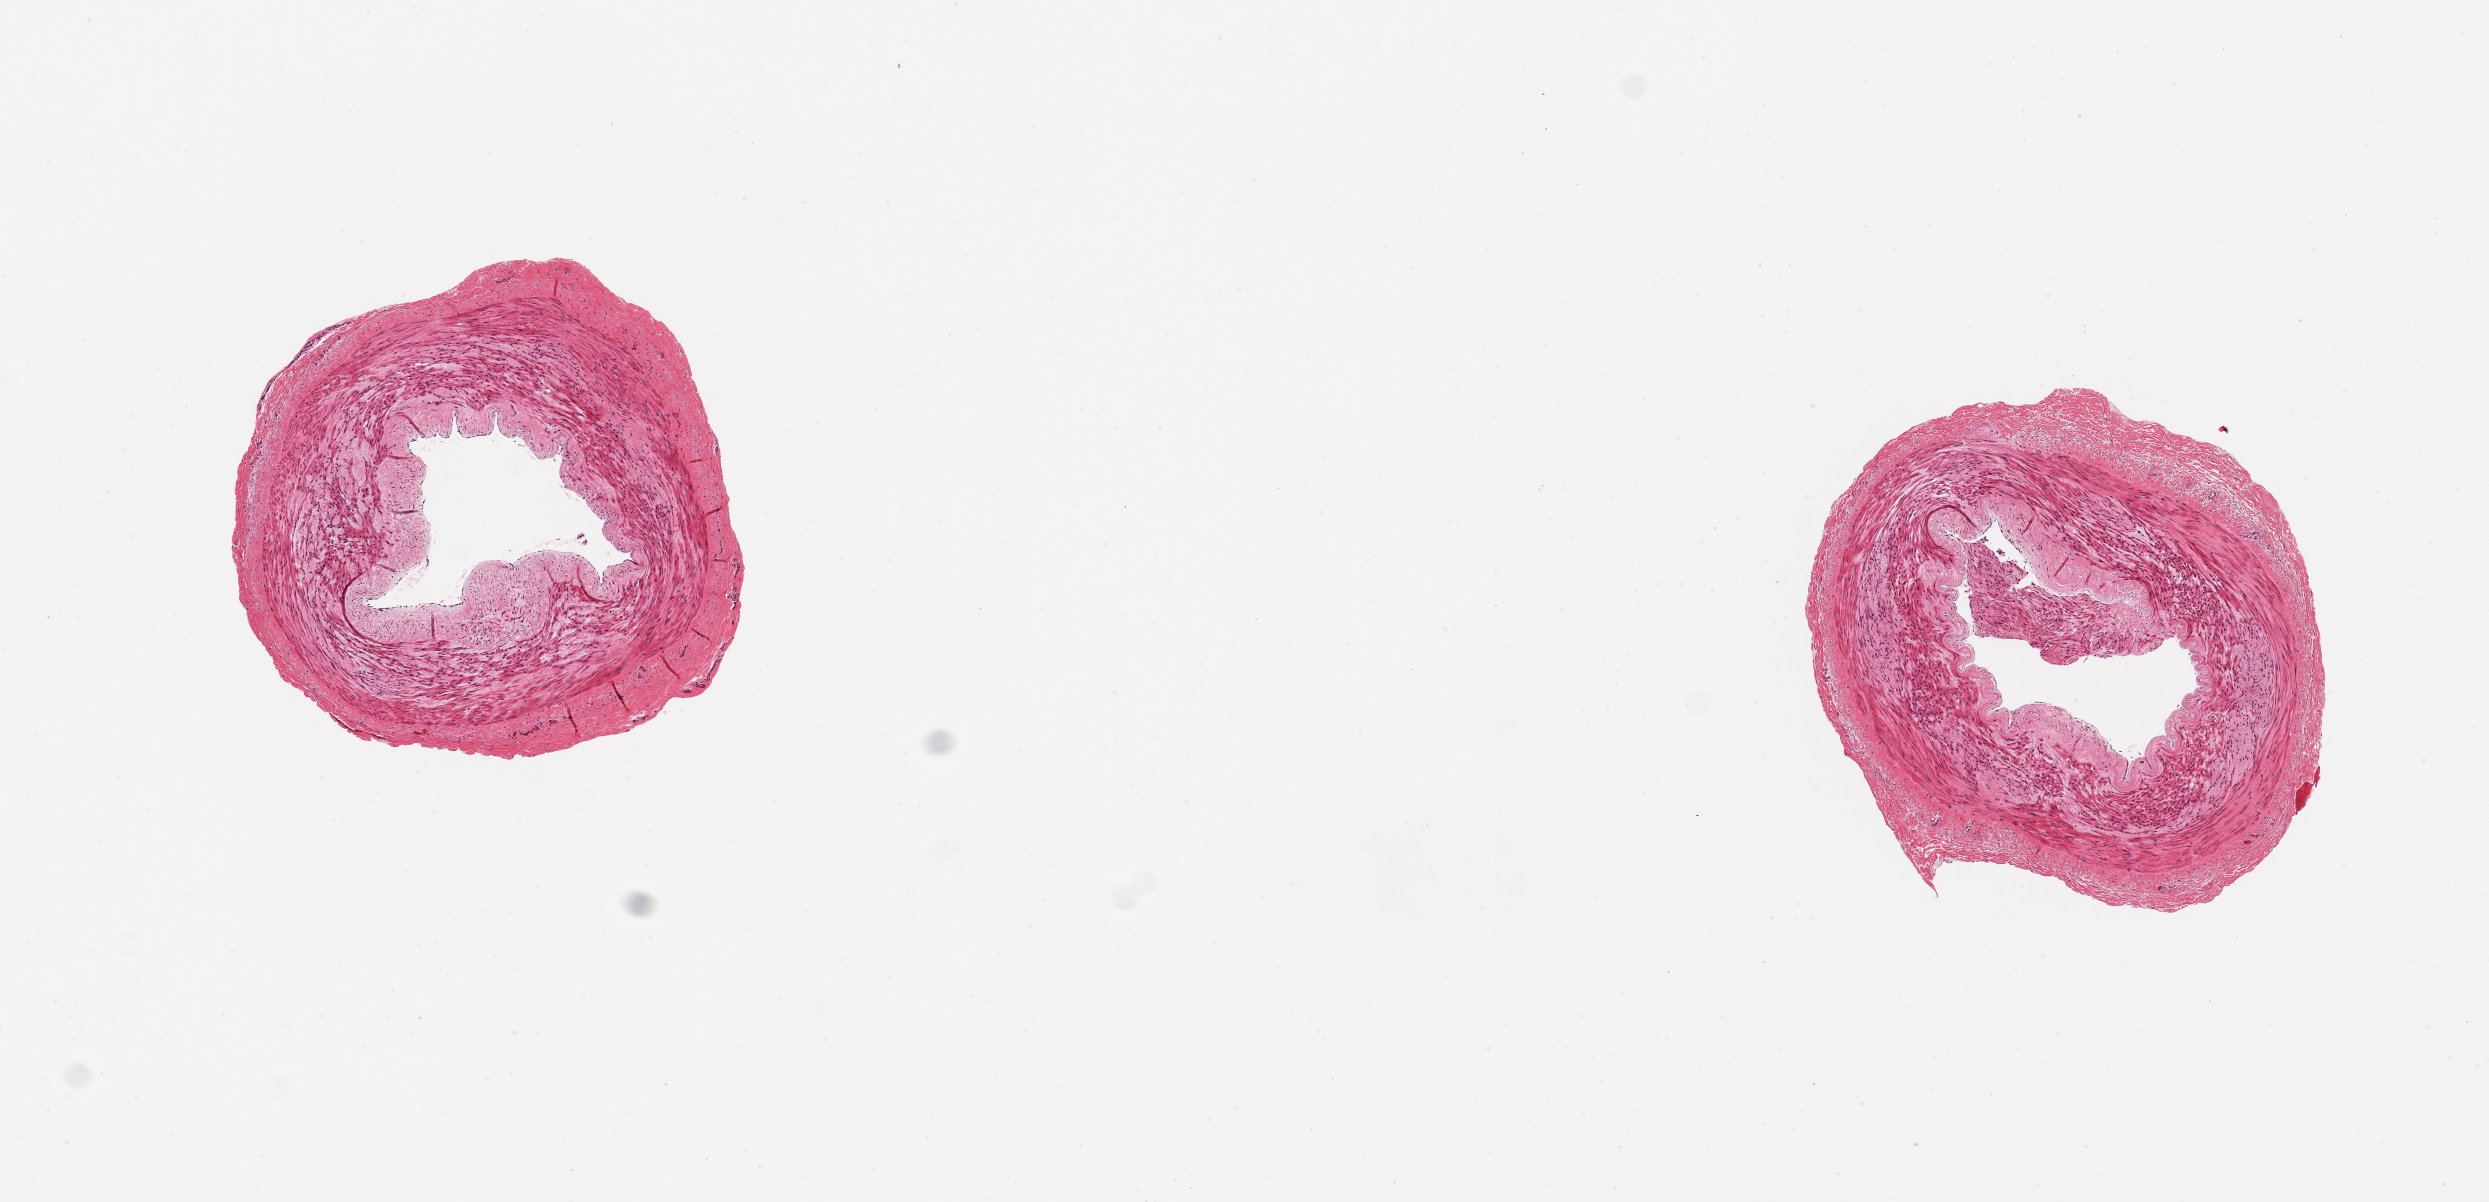
Digitized H&E-stained section, brightfield, a low-resolution overview of the entire scanned area, about 9.8 x 4.8 mm (from a 20x scan). PAXgene-fixed paraffin-embedded (PFPE) section. Target tissue: tibial artery. Donor tissue sample.
Review note (as recorded): 2 pieces; well trimmed; no plaque.